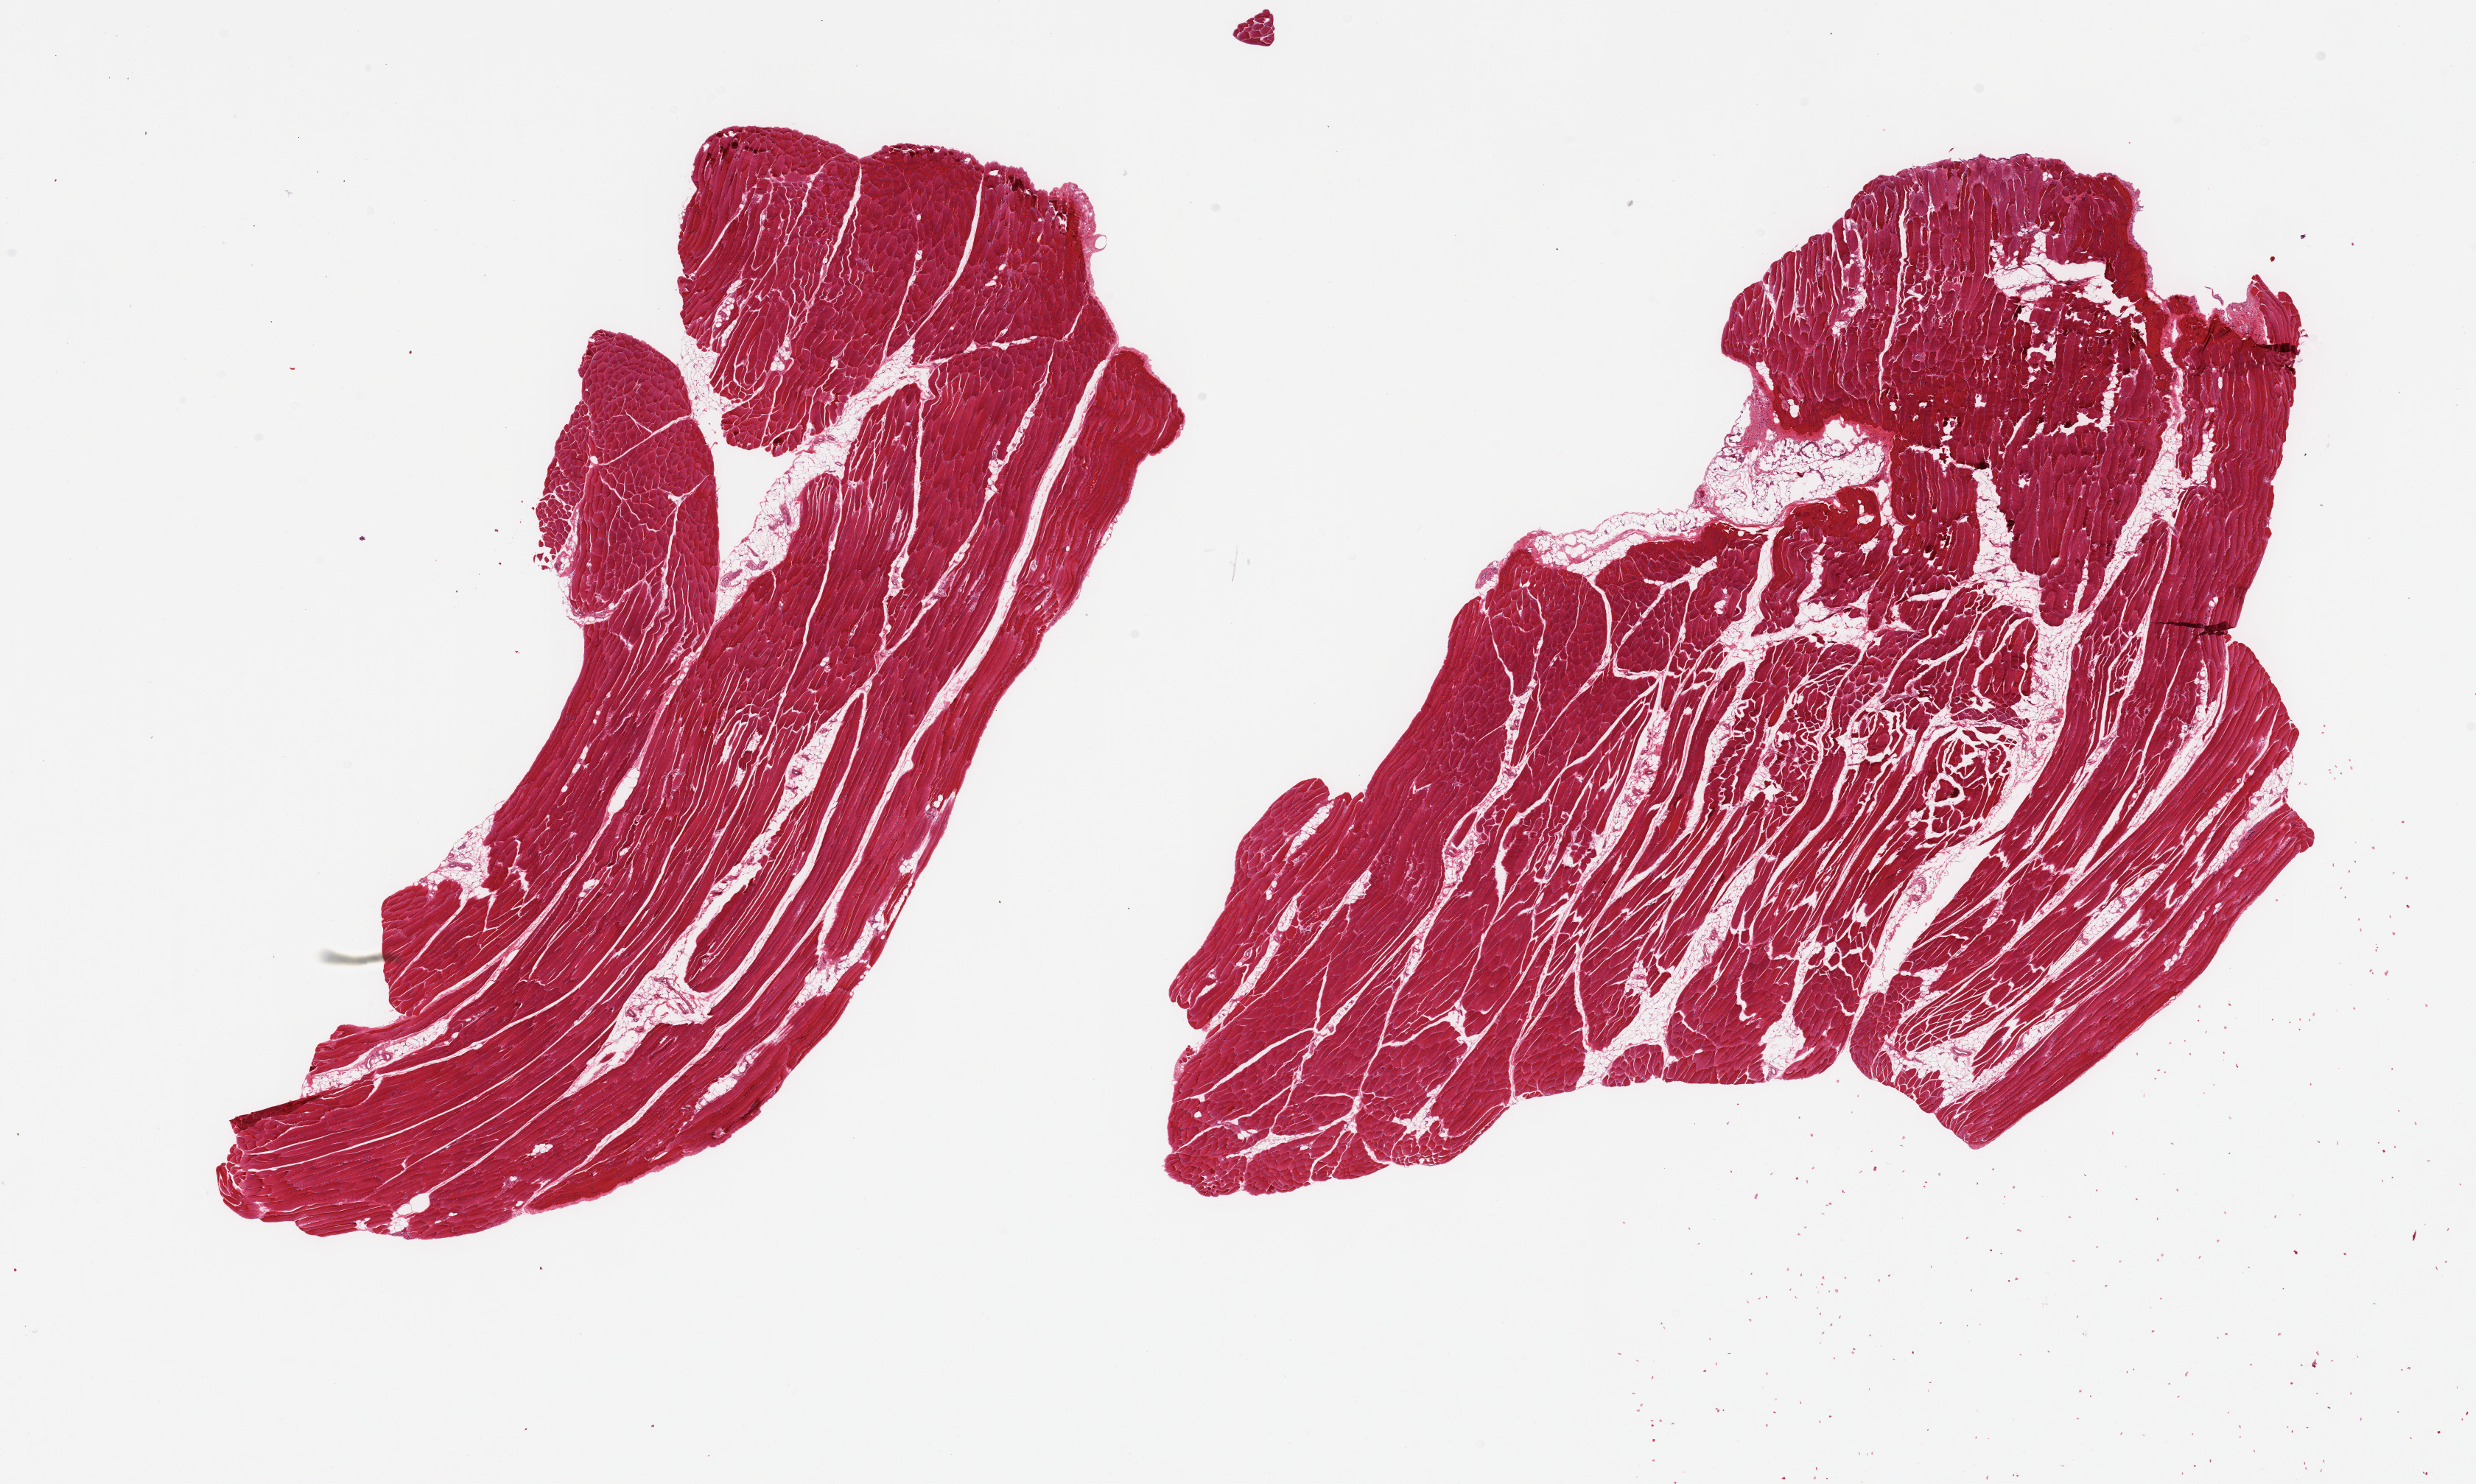
Digitized haematoxylin and eosin-stained section — low-resolution overview of the scanned area, about 26.6 x 15.9 mm (acquisition: 20x scan), PAXgene-fixed paraffin-embedded (PFPE) section, target tissue: skeletal muscle, tissue donor sample. Female donor.
Reviewer comment on this tissue sample: 2 pieces, ~10% interstitial fat.